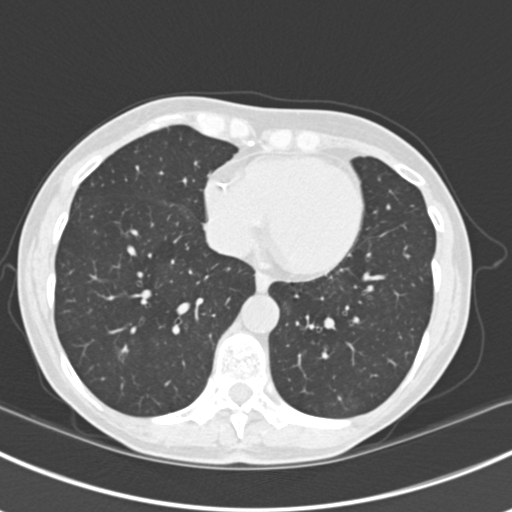
Chest CT (low-dose screening protocol), one axial image, baseline annual screen, lung window (W 1500 / L -600 HU), 2 mm slice thickness, slice 131 of 224 in the series. Female, age 63 years at enrolment. Current smoker at enrolment.
- Expert reader's lesion annotation, bounding box (x1, y1, x2, y2) in pixels: (97, 316, 148, 367).
- The screening reader recorded 10 non-calcified nodules or masses ≥4 mm on this exam (right lower lobe, right lower lobe, left lower lobe, left lower lobe, right middle lobe, right lower lobe, left lower lobe, left upper lobe, right upper lobe, left upper lobe); which of them this box marks is not recorded.
- Official screen result: positive, change unspecified: nodule(s) >= 4 mm or enlarging nodule(s), mass(es), or other non-specific abnormalities suspicious for lung cancer.
- Lung cancer was diagnosed 751 days after this screen (after the third annual screen): bronchiolo-alveolar adenocarcinoma, NOS, right upper lobe, right middle lobe, right lower lobe, left upper lobe, left lower lobe, moderately differentiated (G2), stage IV (AJCC 6th edition).